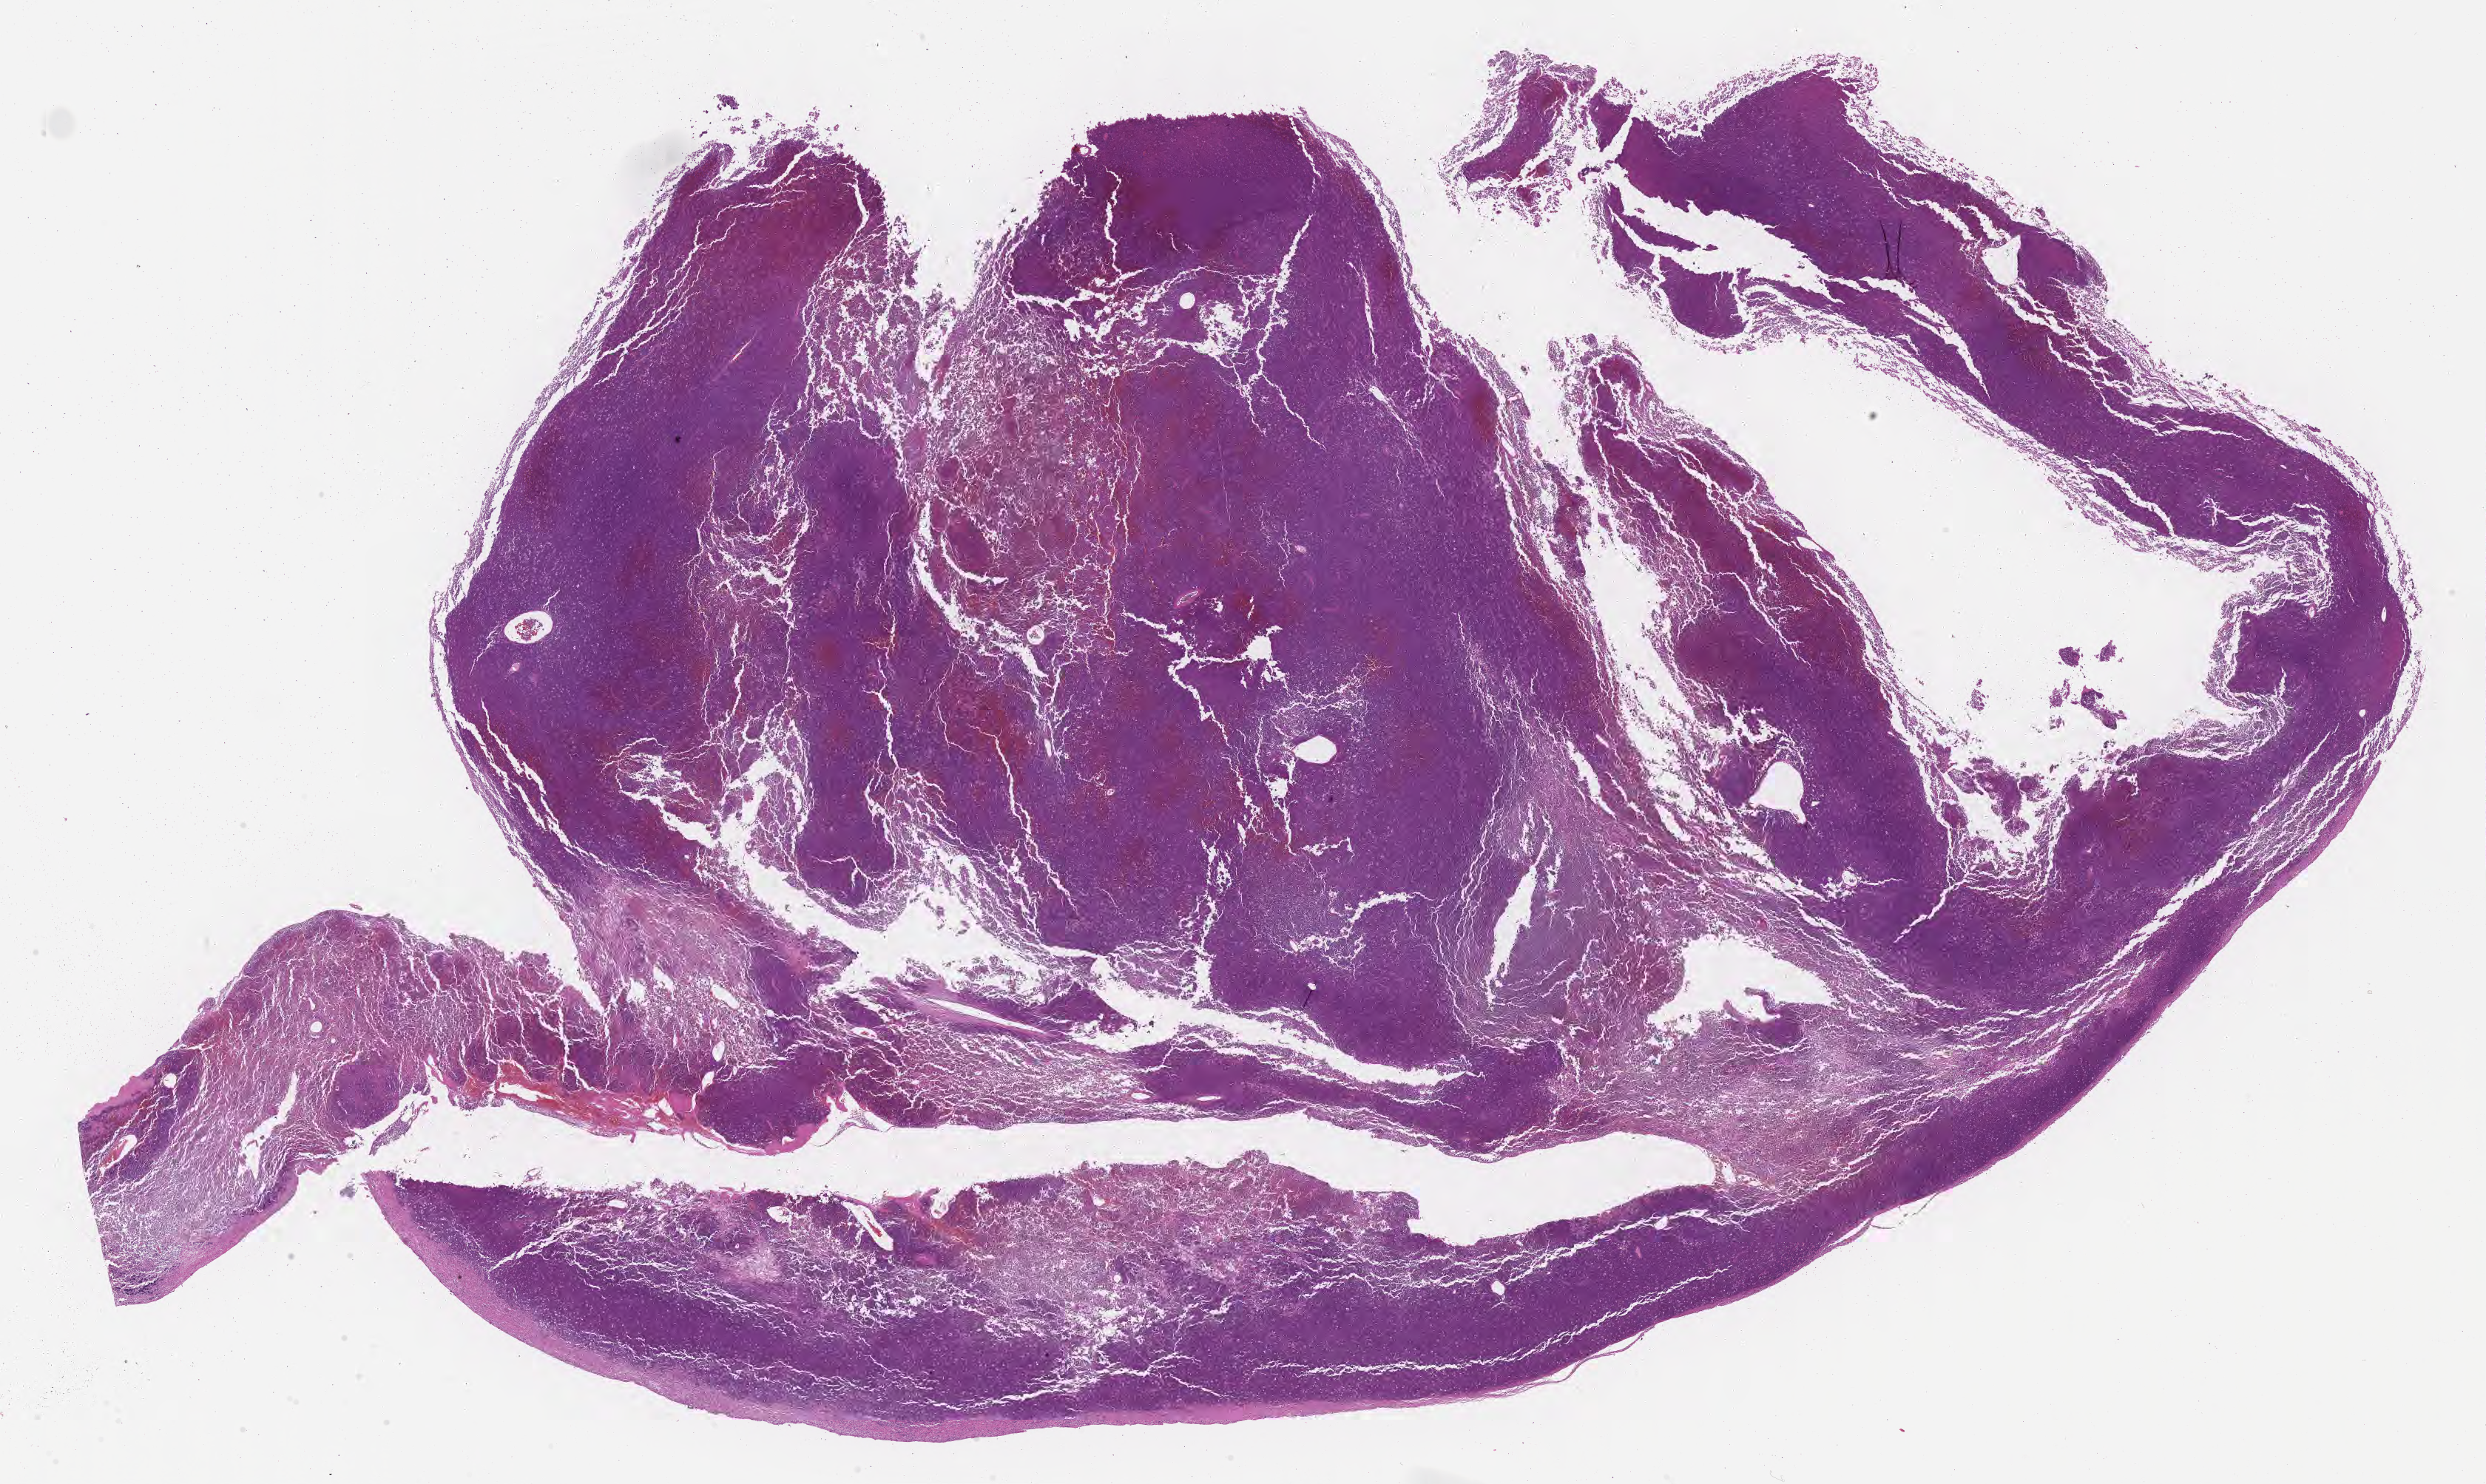
Whole-slide image, hematoxylin and eosin (H&E) stain, shown as a low-resolution overview of the whole scanned area (about 27.2 x 16.2 mm). FFPE section. Primary tumor. Patient: female, age at initial diagnosis 3 years. Slide review estimates, as recorded: tumor cells 85%, tumor nuclei 90%, stromal cells 5%, necrosis 0%, normal cells 10%. Infiltration values recorded for this section: lymphocyte infiltration 70%, monocyte infiltration 15%, neutrophil infiltration 0%.
- Ann Arbor stage (patient): Stage IV
- histologic diagnosis: Burkitt lymphoma, NOS